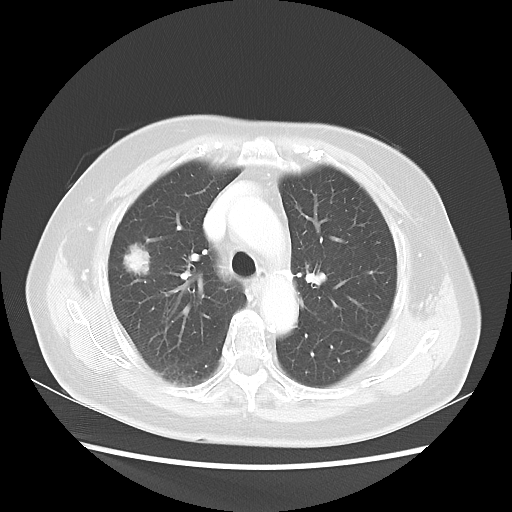
Chest CT, one axial slice. Slice 33 of 48 in the series (ordered by position). 100 kVp. Lung window (W 1500 / L -600 HU). 5 mm slice thickness. 512 × 512 image matrix, field of view 360 × 360 mm. Patient: female, 75 years. Case-level facts recorded for this patient, not image findings: clinical TNM (as recorded): T1c N0 M0.
Structures marked on this image (bounding box drawn by a radiologist):
- lung tumour (recorded histology: adenocarcinoma): bounding box [x1, y1, x2, y2] px = [119, 238, 162, 289]